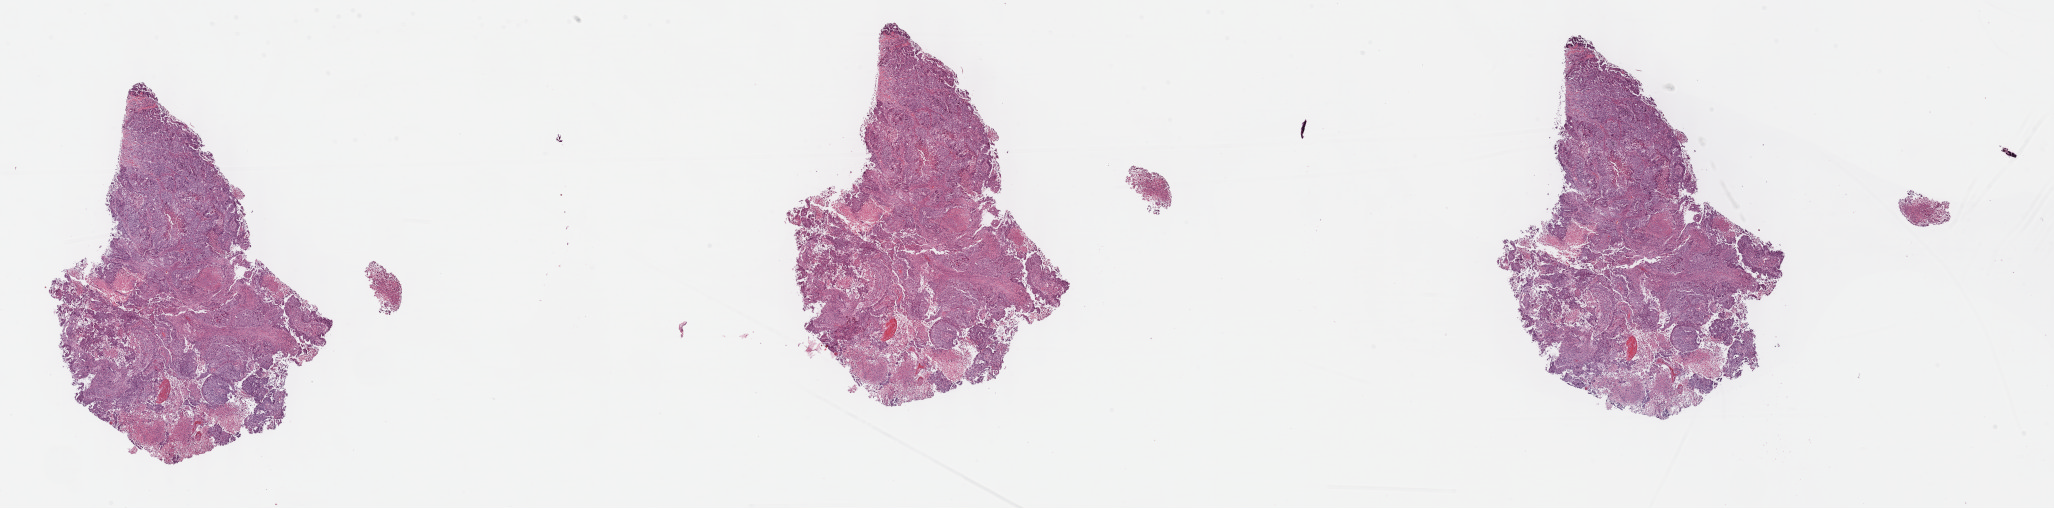
Whole-slide histology image, Hematoxylin and eosin (H&E) stained — shown as a low-resolution overview of the whole scanned area (about 33.2 x 8.2 mm, slide scanned at 40x), formalin-fixed paraffin-embedded (FFPE) diagnostic section, sample: primary tumour, uterus. Patient: female, age at initial diagnosis 74 years. Histologic grade: G3 (poorly differentiated).
• FIGO stage: IB
• diagnosis: Endometrioid adenocarcinoma, NOS (endometrium)